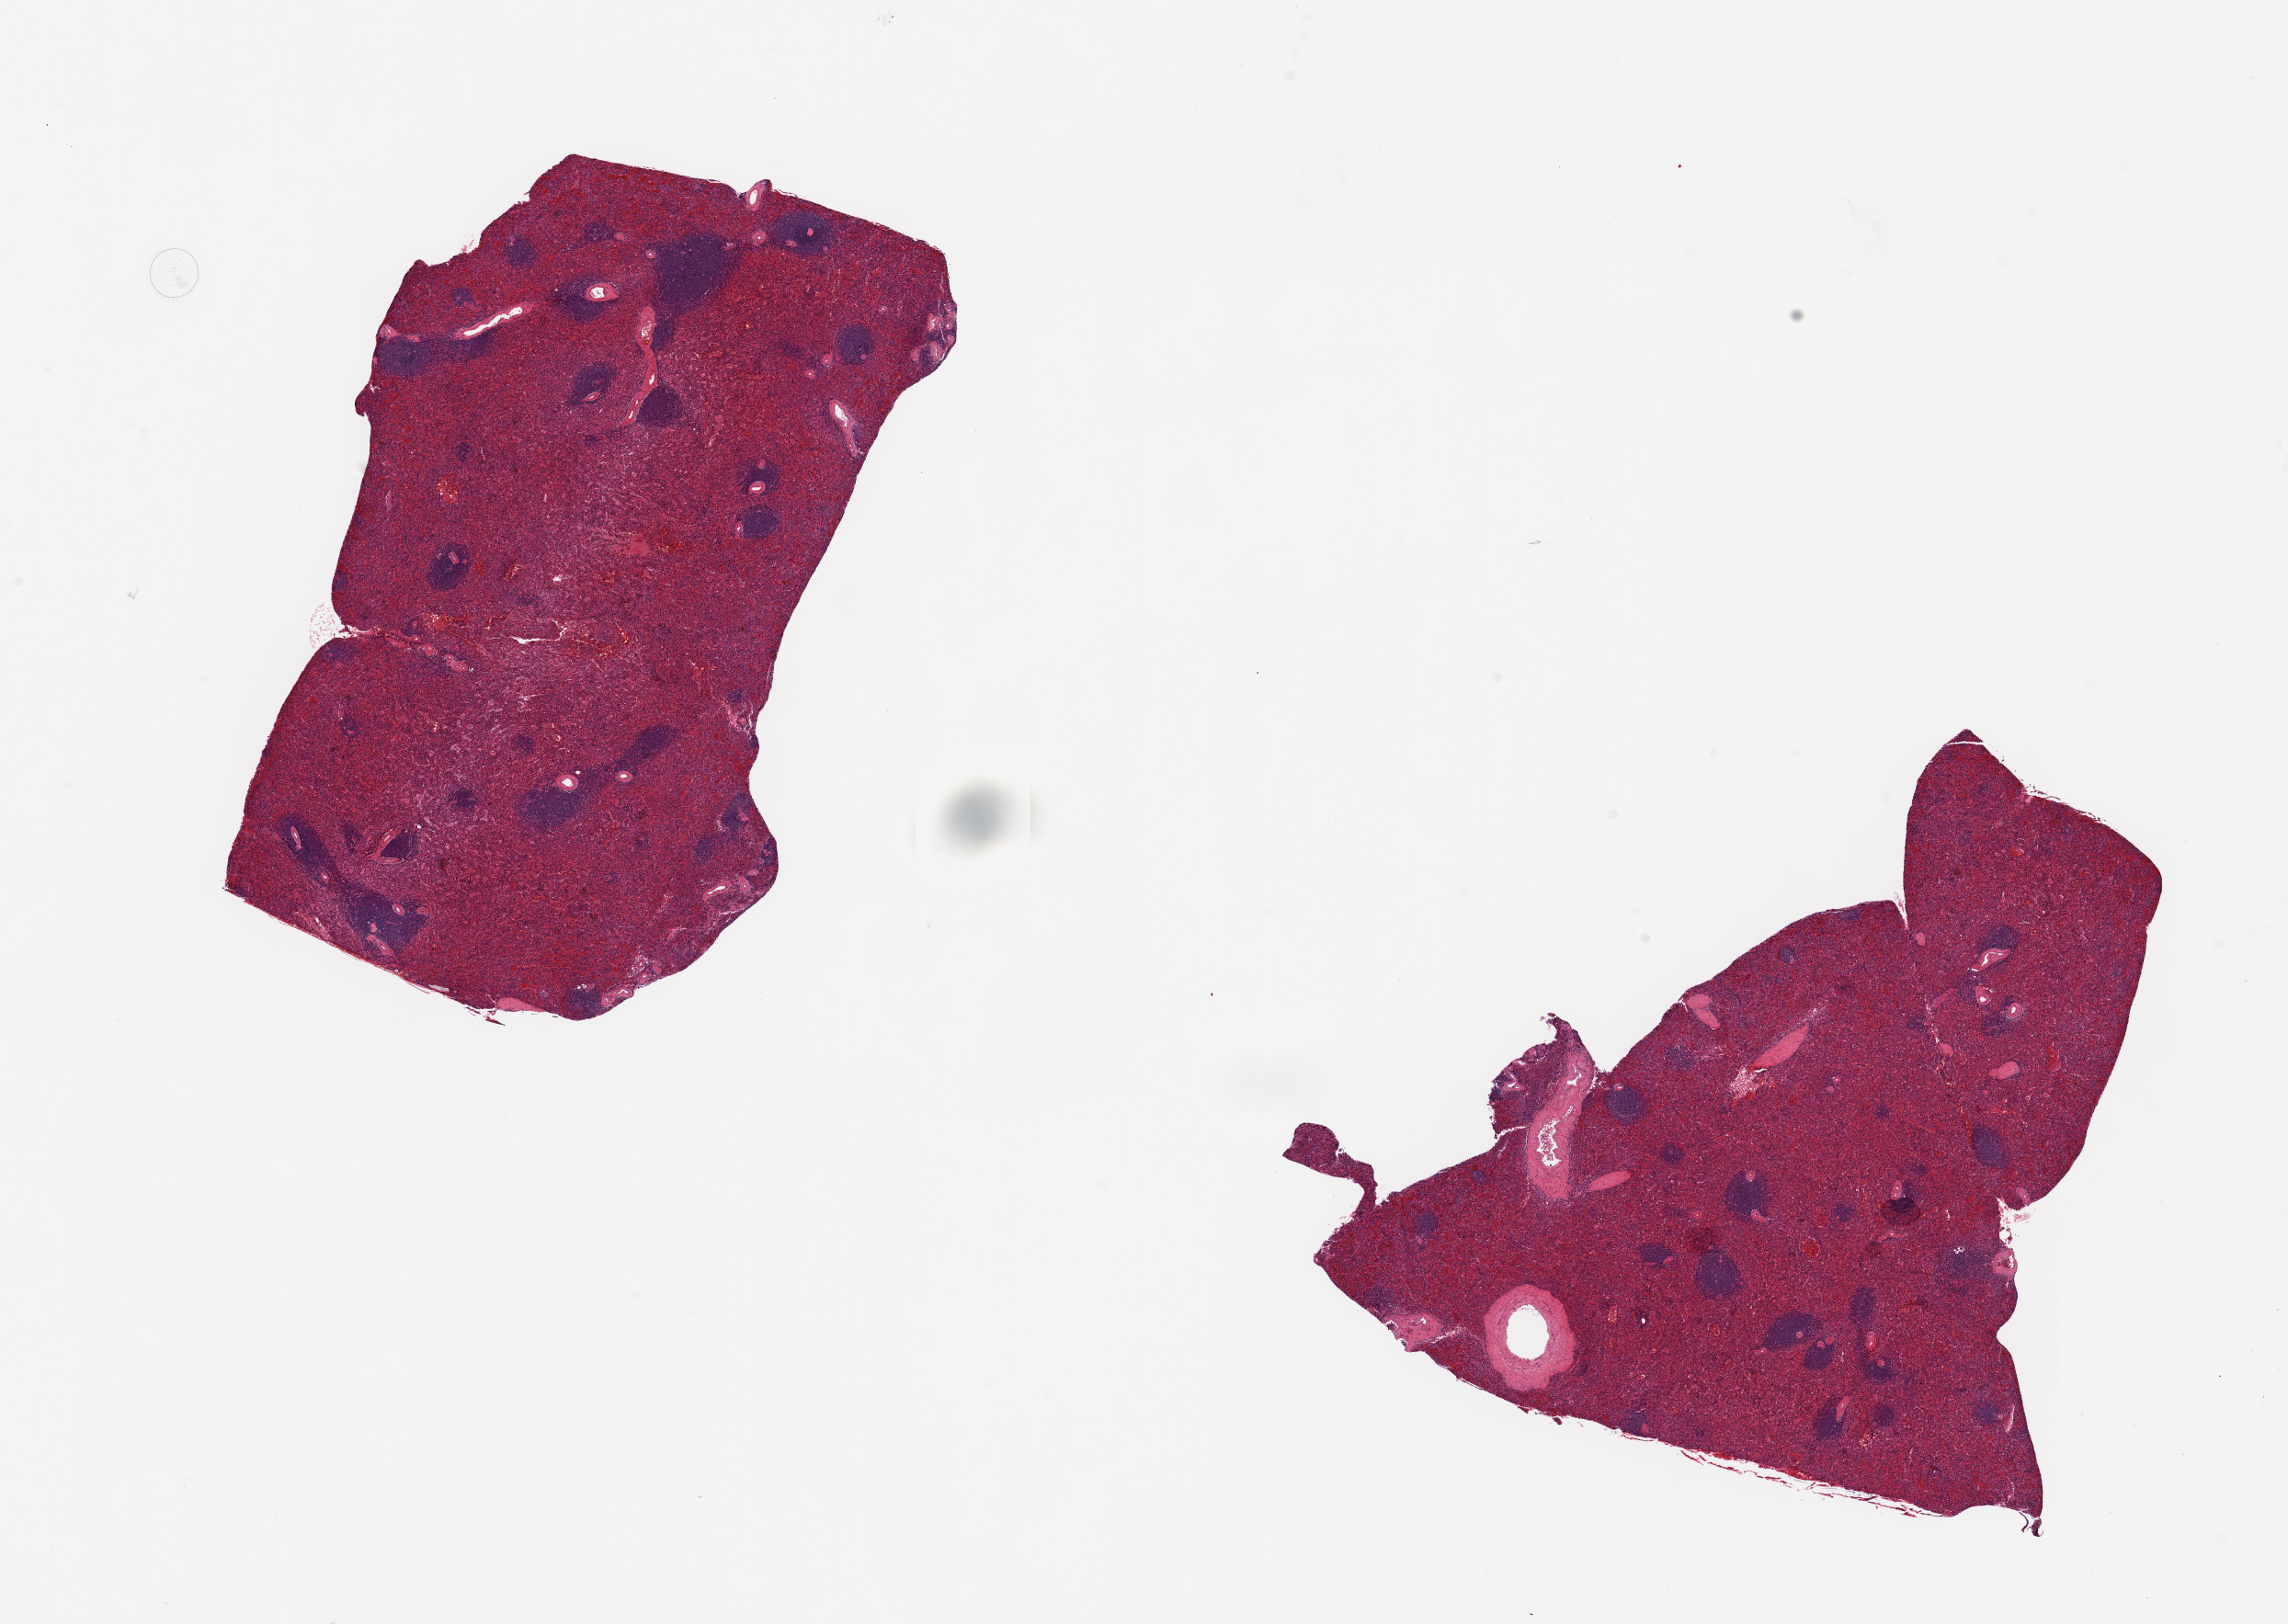
Digitized H&E-stained section, shown as a low-resolution overview of the whole scanned area (about 19.7 x 14.0 mm); PAXgene-fixed, paraffin-embedded tissue; sampled site (target tissue): spleen; donor tissue sample. Donor: male.
Pathologist's review note for this sample: 2 pieces 6x6 & 7x4 mm; moderately congested.